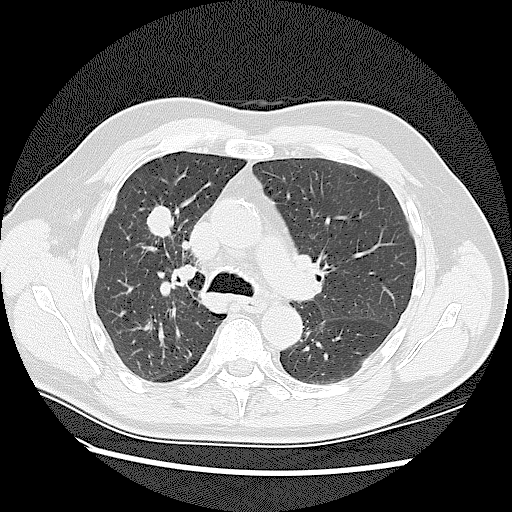
Low-dose screening chest CT, one axial slice; position 82 of 128 along the scan axis; 120 kVp; lung window (W 1500 / L -600 HU); 512 × 512 image matrix, field of view 360 × 360 mm.
Annotated regions visible in this slice (manually delineated by an expert):
- lesion 1 (tumor, upper lobe of right lung): box from (x=147, y=204) to (x=174, y=238) px